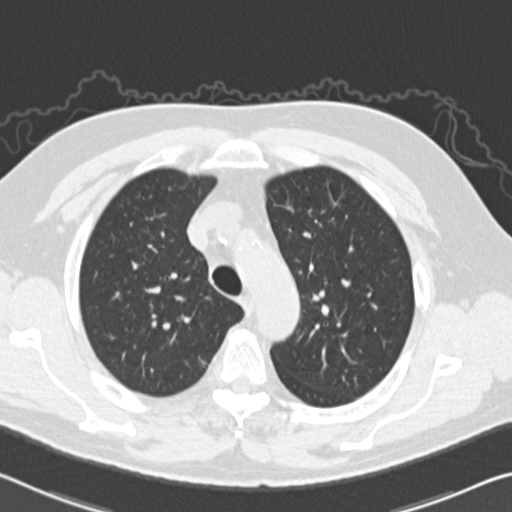
Chest CT (low-dose screening protocol), one axial image. Baseline screening round. Lung window (W 1500 / L -600 HU). 2 mm slice thickness. Slice 35 of 151 in the series. 512 × 512 image matrix. Male participant, aged 64 years at enrolment.
Expert-annotated lung lesion, bounding box (x1, y1, x2, y2) in pixels: (183, 344, 229, 383). Screening reader's record for this exam (one nodule recorded; not confirmed to be the boxed lesion): non-calcified nodule or mass ≥4 mm, right upper lobe, 10 × 8 mm, spiculated (stellate) margins, soft tissue attenuation. Later outcome: lung cancer diagnosed 99 days after this screen — adenocarcinoma, NOS, right upper lobe, poorly differentiated (G3), stage IA (AJCC 6th edition), 11 mm at pathology.